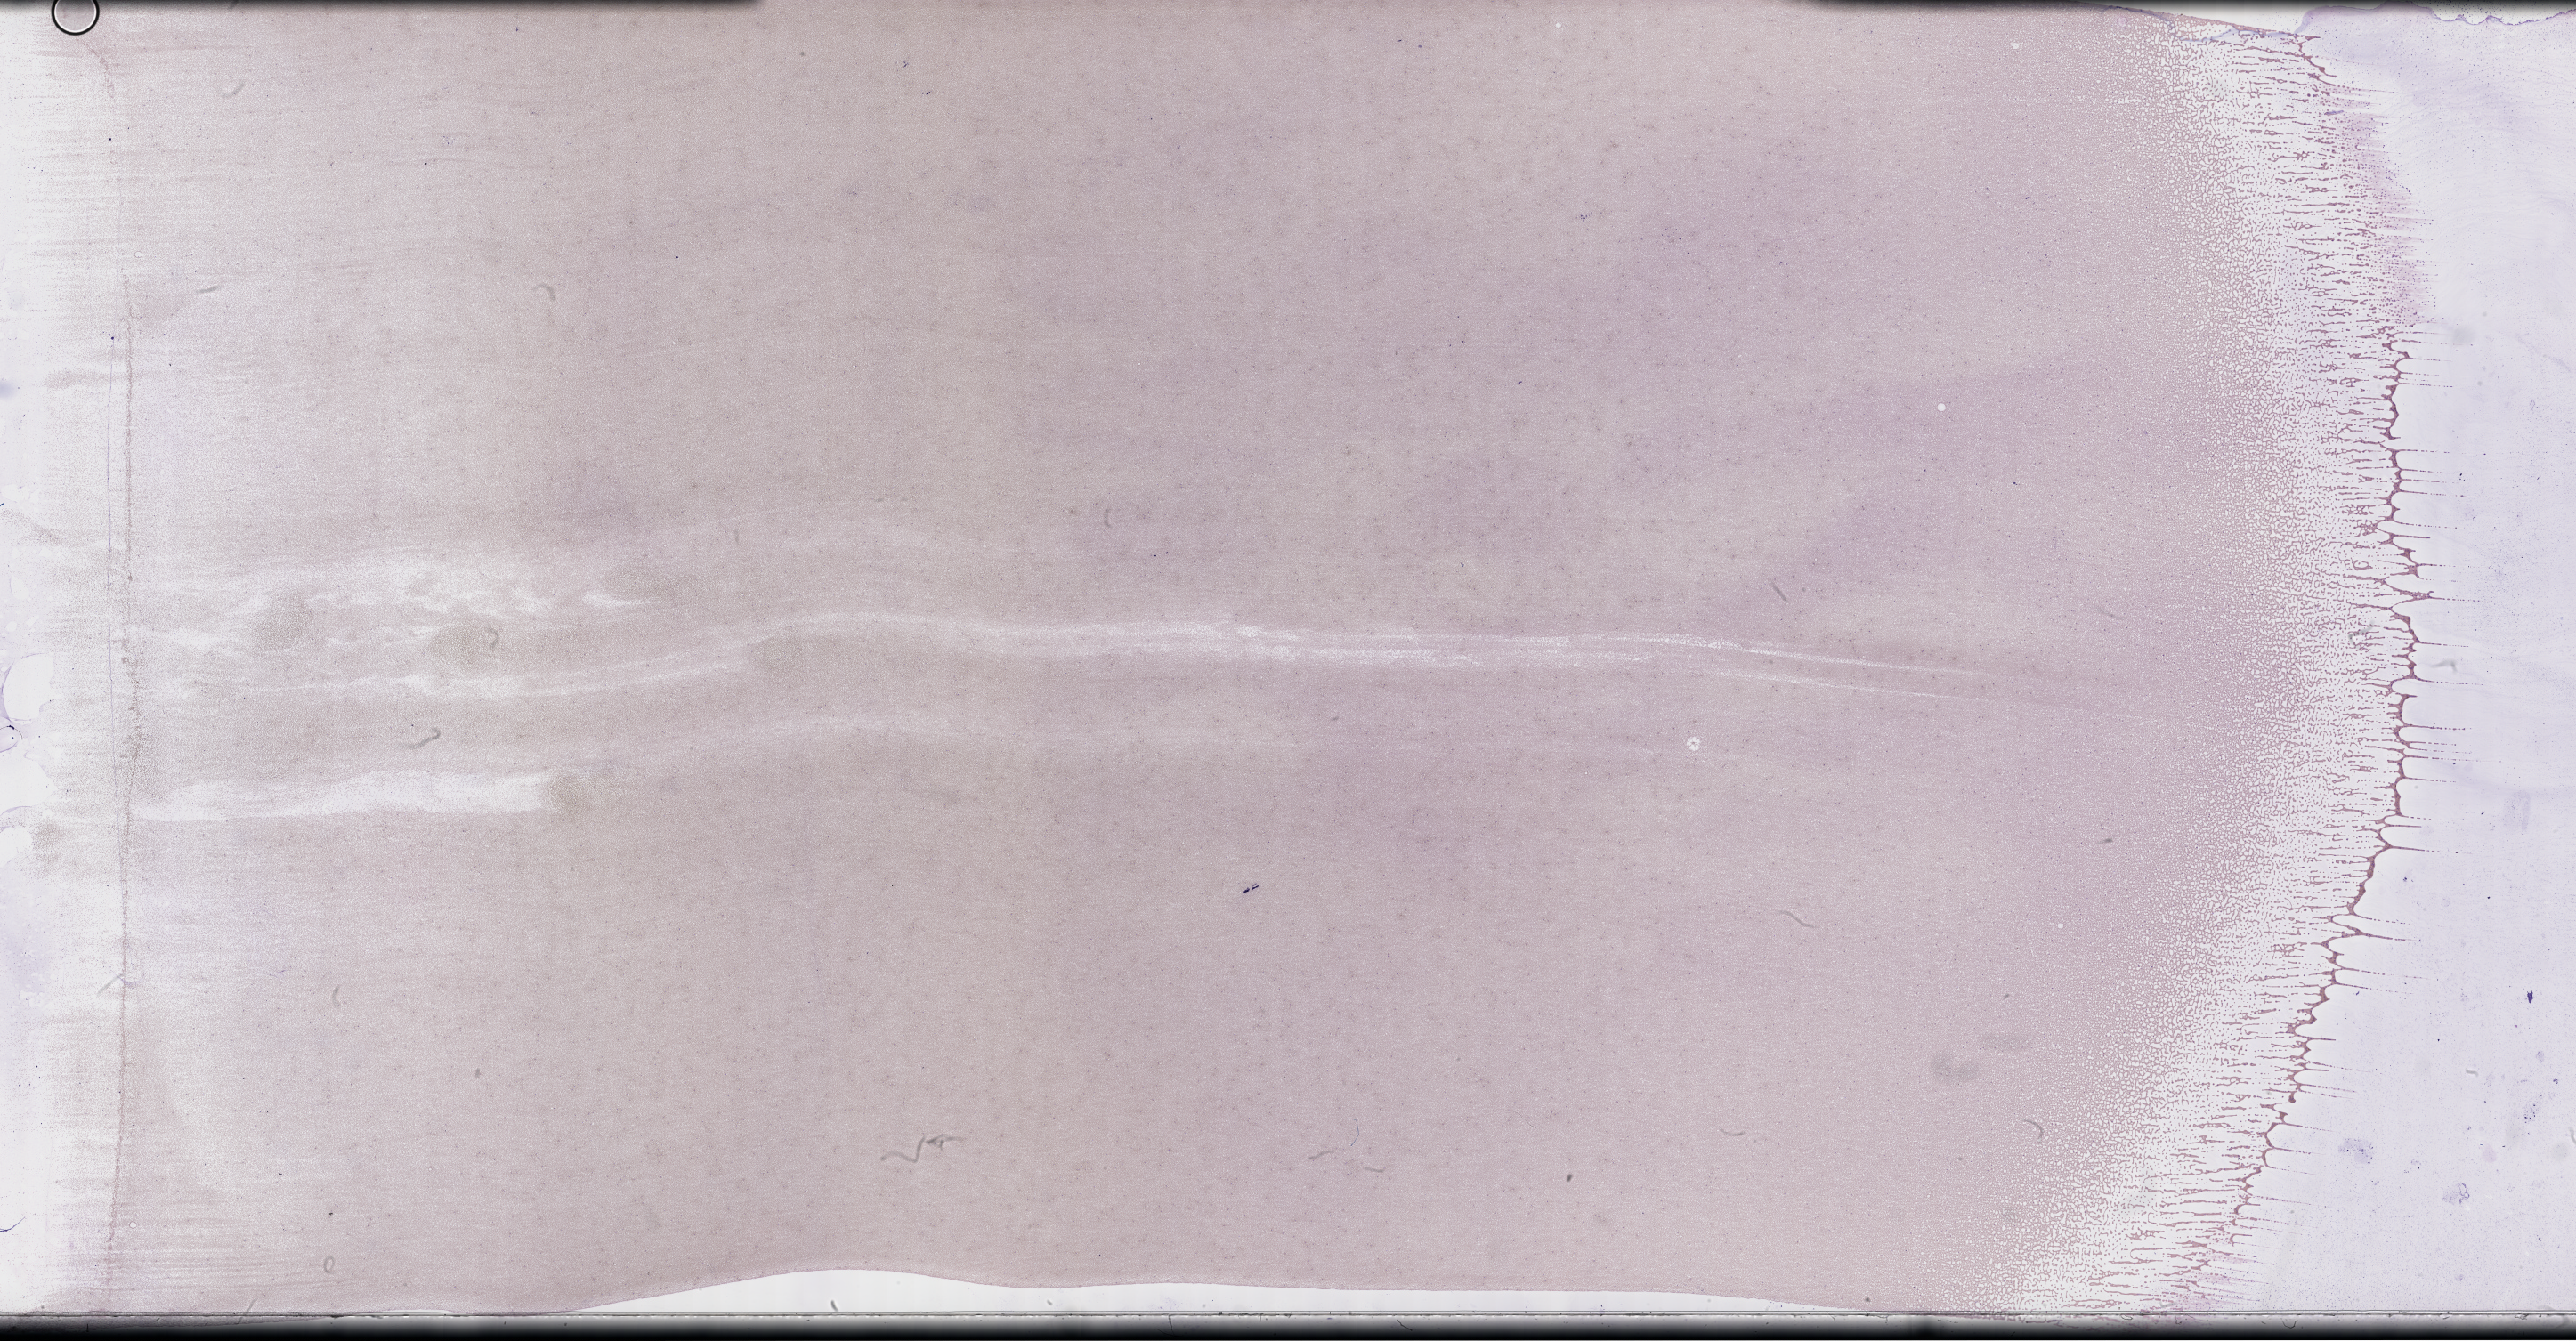
Whole-slide image of a whole blood smear, Wright-Giemsa stain, a low-resolution overview of the entire scanned area, about 46.7 x 24.3 mm; EDTA-anticoagulated smear; collected on treatment. Patient sex: female.
Patient diagnosis: Plasma Cell Myeloma.